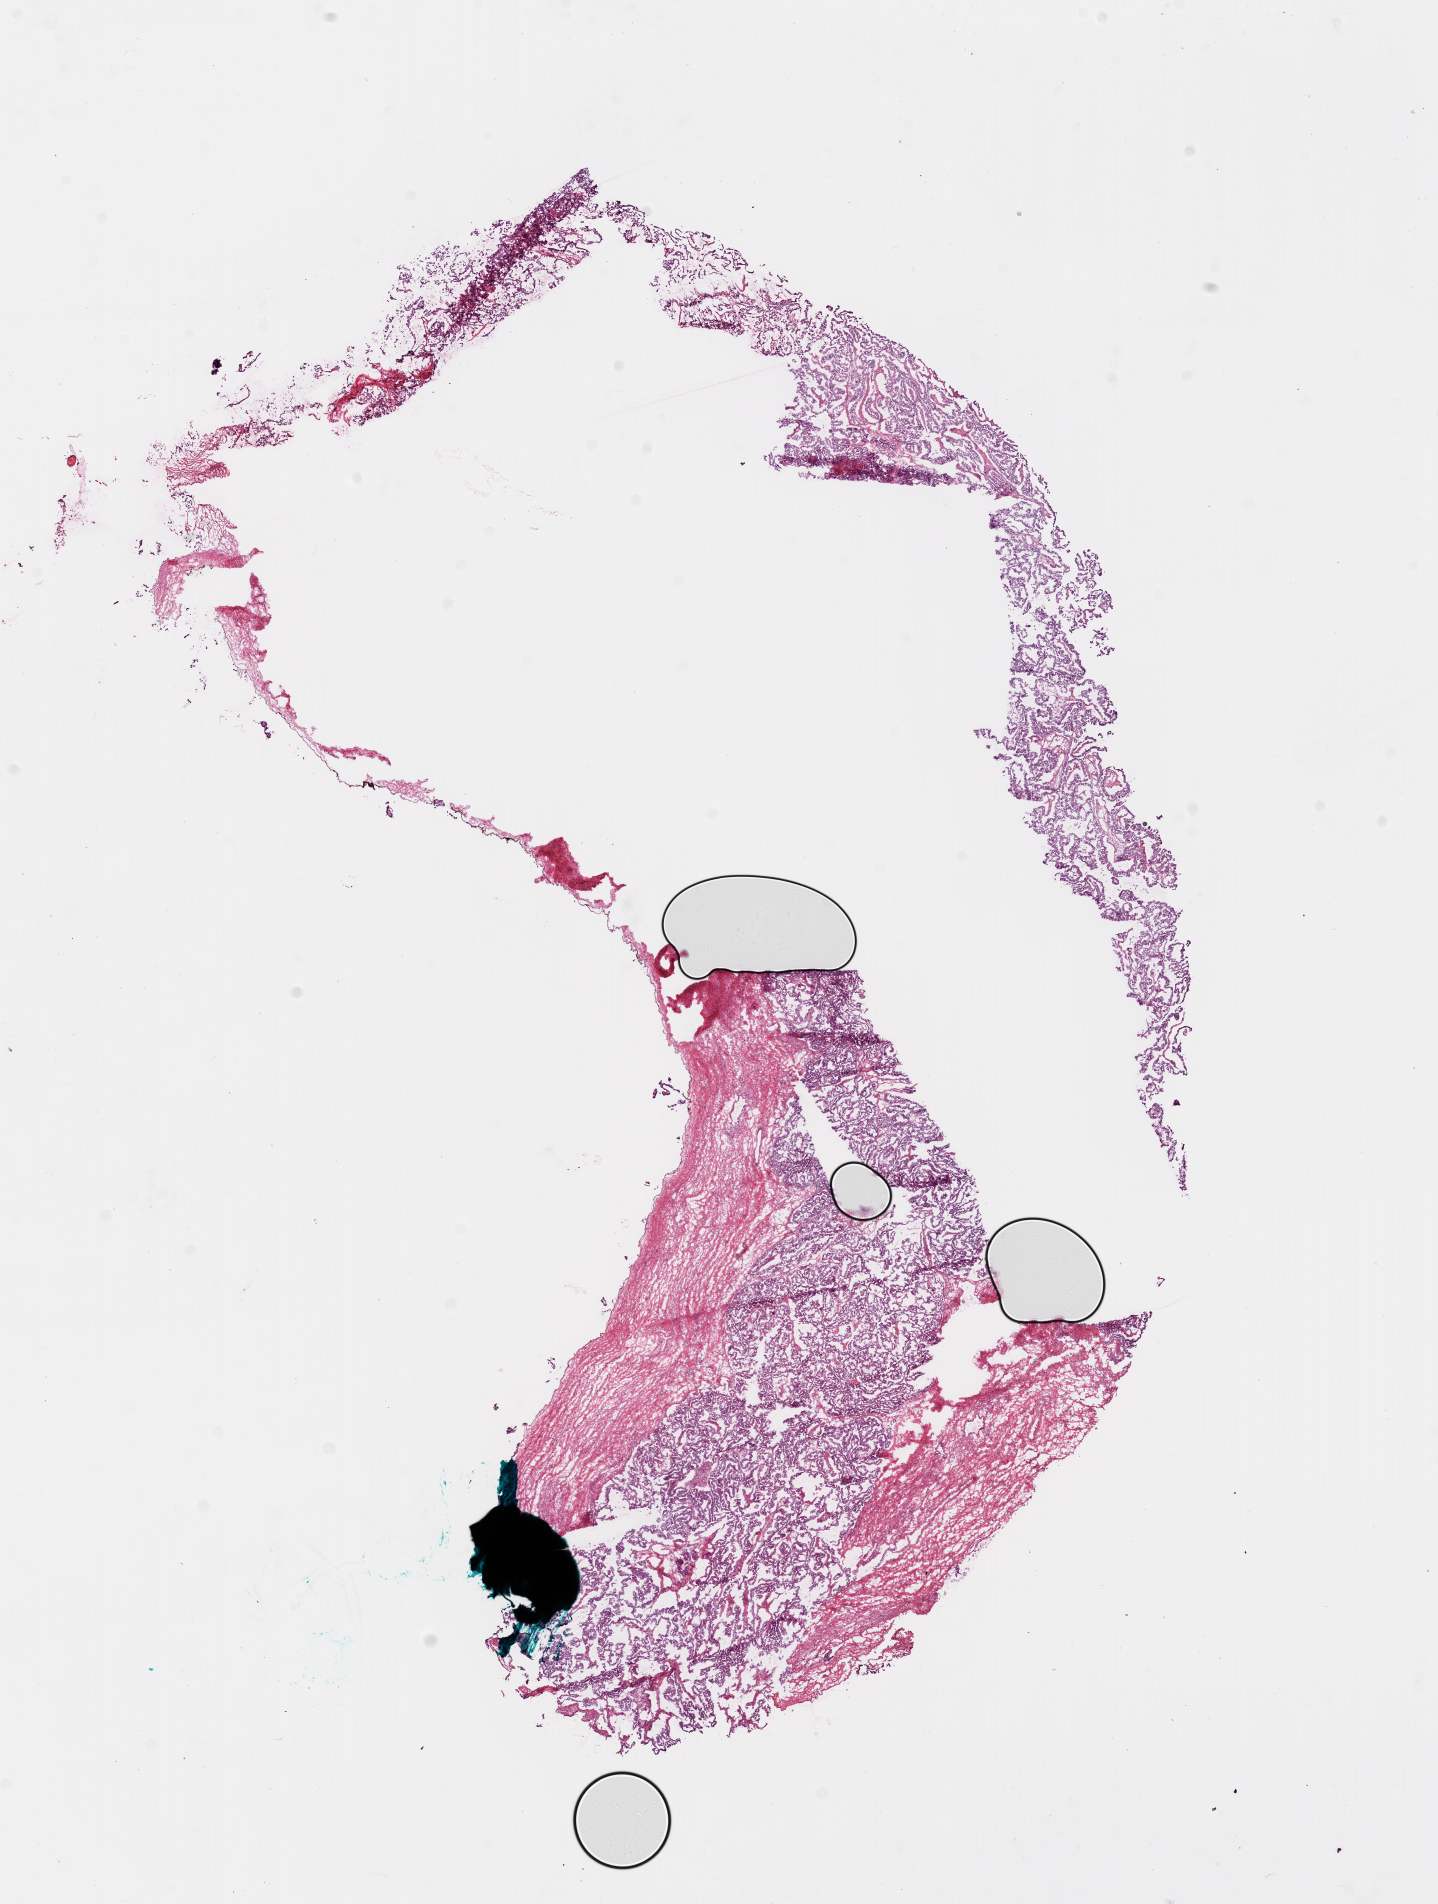
Whole-slide histology image, H&E-stained — a low-resolution overview of the entire scanned area, about 11.6 x 15.4 mm. Frozen section. Primary tumour sample from the ovary. Female patient; age at initial diagnosis 53 years. Histologic grade: G3 (poorly differentiated). Pathologist review of this section (percent, as recorded): tumour cells 75%, tumour nuclei 85%, normal cells 0%, stromal cells 25%, necrosis 0%. Inflammatory infiltration, as recorded: lymphocyte infiltration 100%.
• laterality: bilateral
• diagnosis: Serous cystadenocarcinoma, NOS
• FIGO stage: IIIC